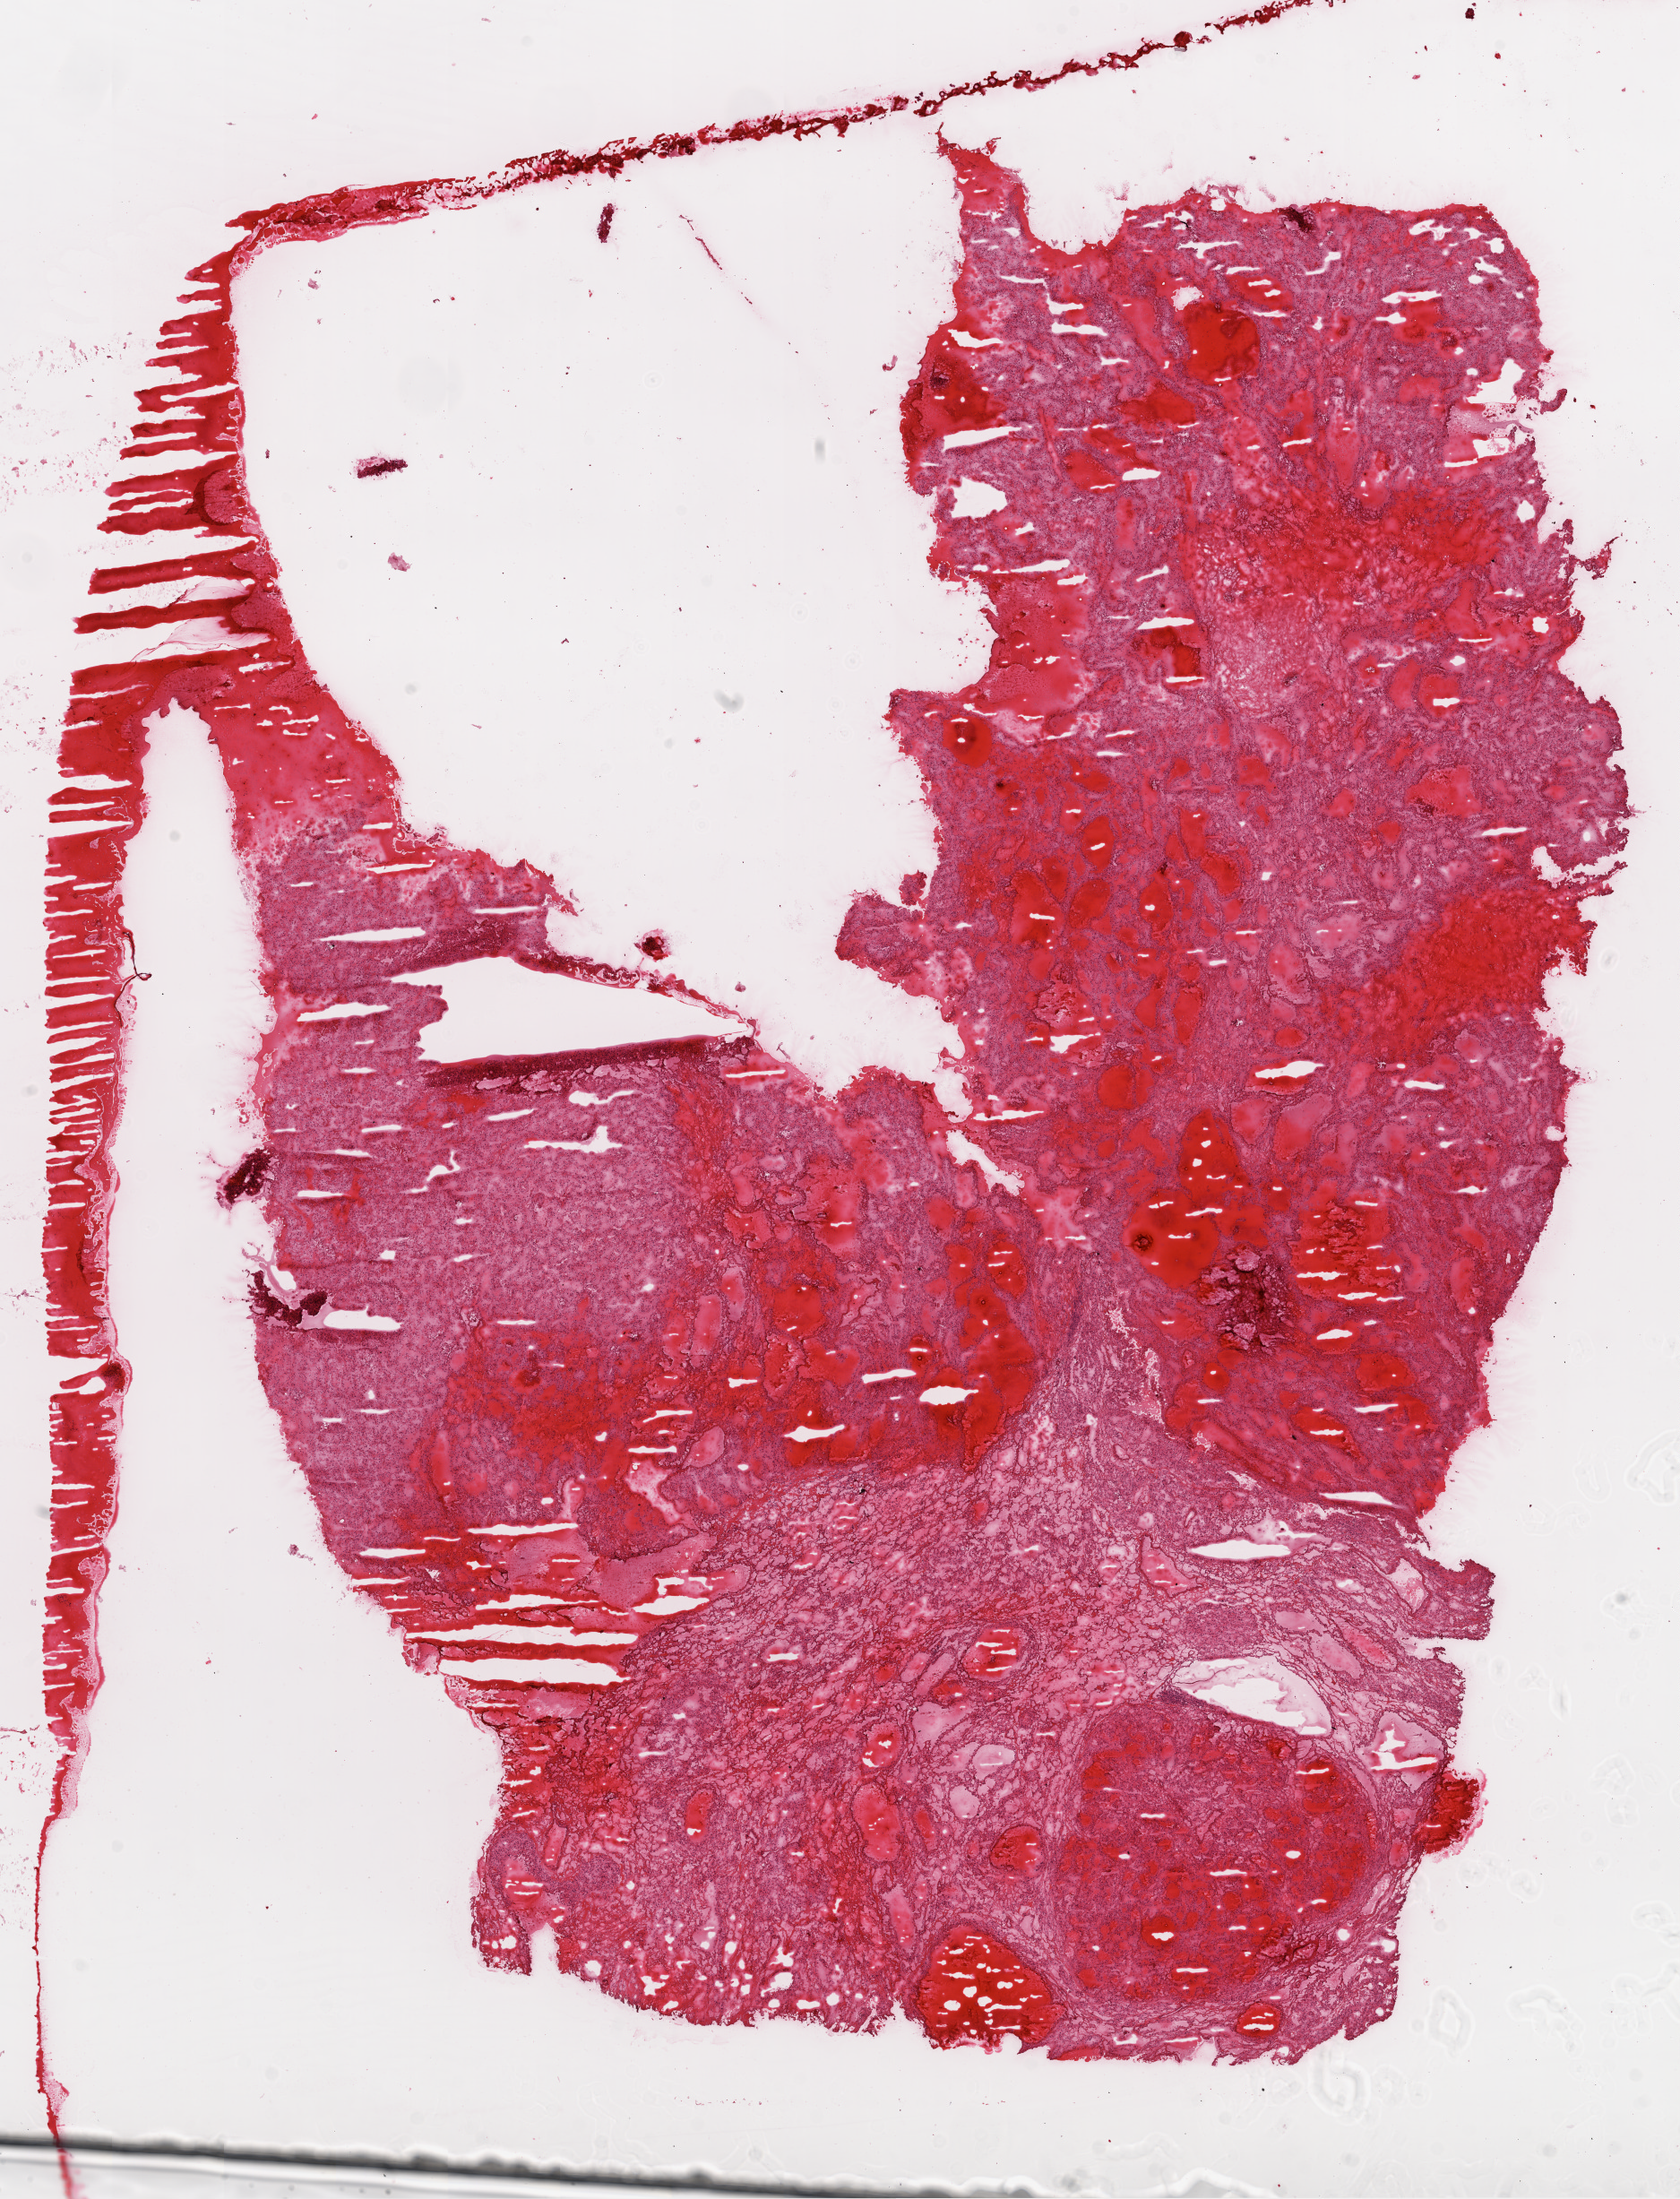
Whole-slide histology image, Hematoxylin and eosin (H&E) stained — shown as a low-resolution overview of the whole scanned area (about 15.0 x 19.7 mm, acquisition: 20x scan), frozen section from the top of the tissue portion, primary tumour sample from the kidney. Male patient; age at initial diagnosis 54 years. Histologic grade: G2 (moderately differentiated). Slide review estimates, as recorded: tumour cells 90%, tumour nuclei 85%, normal cells 0%, stromal cells 10%, necrosis 0%.
* pathologic diagnosis: Clear cell adenocarcinoma, NOS
* AJCC pathologic stage: I